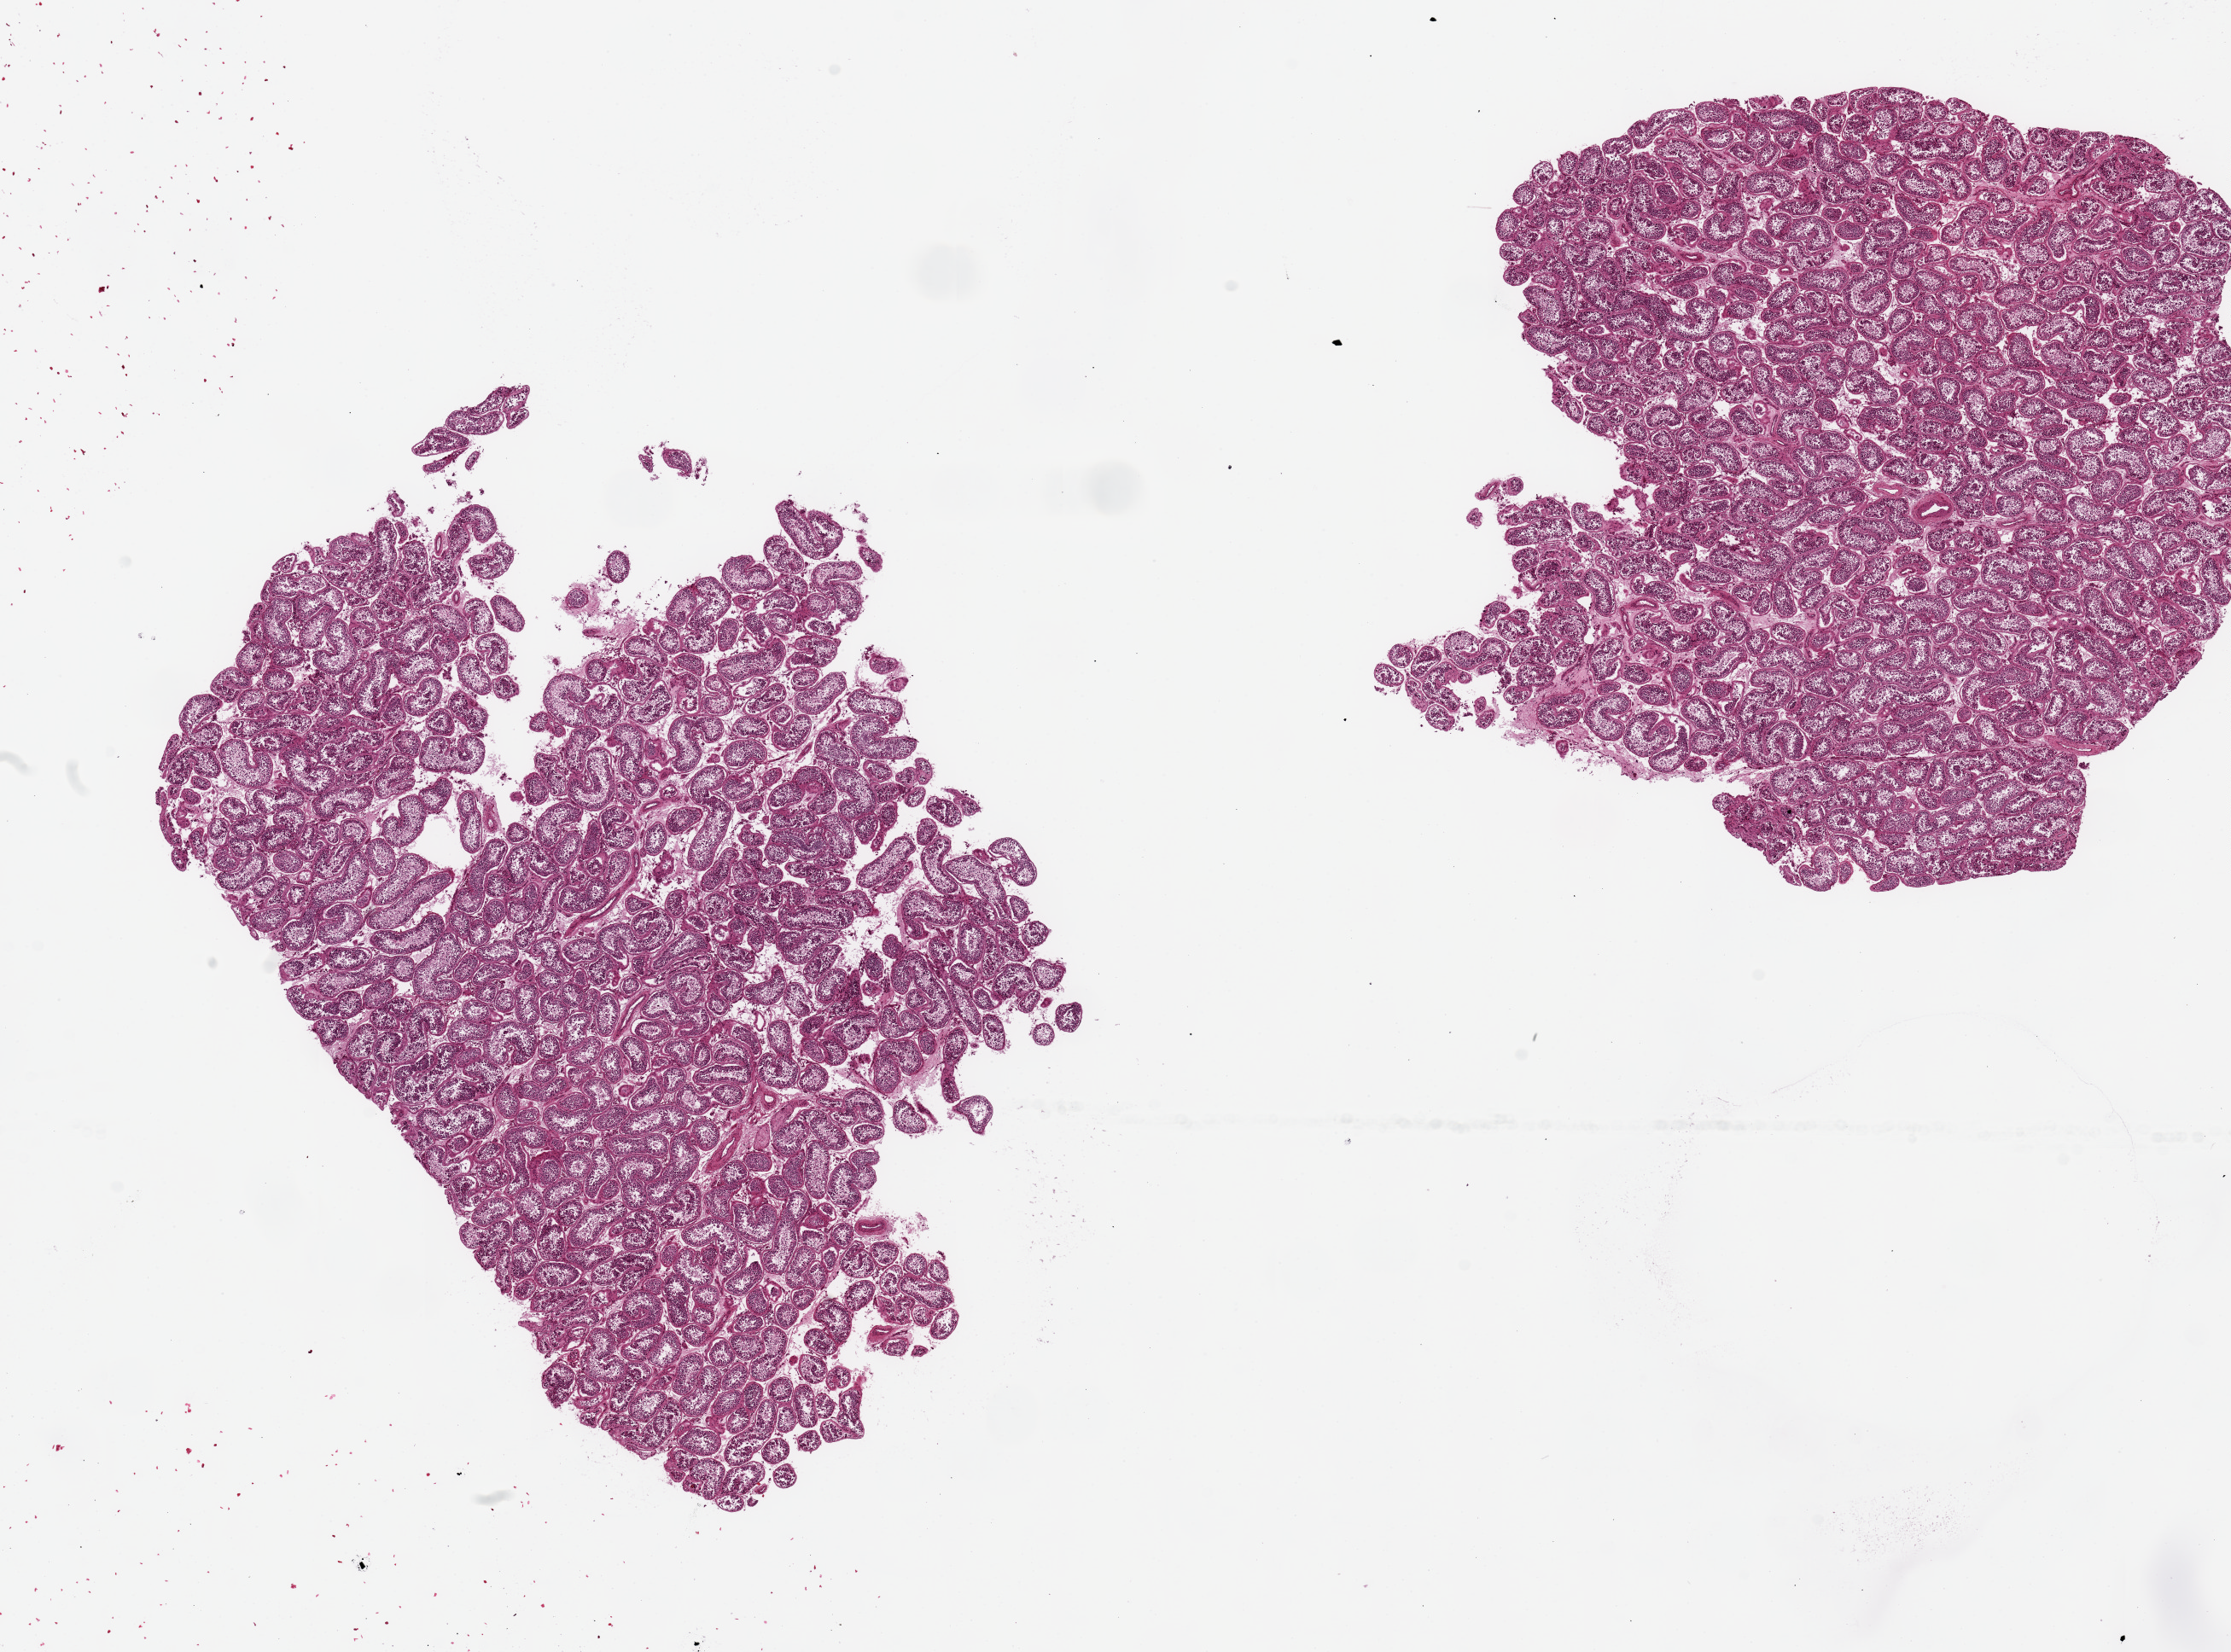
Hematoxylin and eosin (H&E) whole-slide image, low-resolution overview of the scanned area, about 20.7 x 15.3 mm (from a 20x scan). PAXgene-fixed, paraffin-embedded tissue. Sampled site (target tissue): testis. Donor tissue sample. Male donor.
- pathologist's review note for this sample: 2 pieces ~8x6mm; spermatogenesis is present